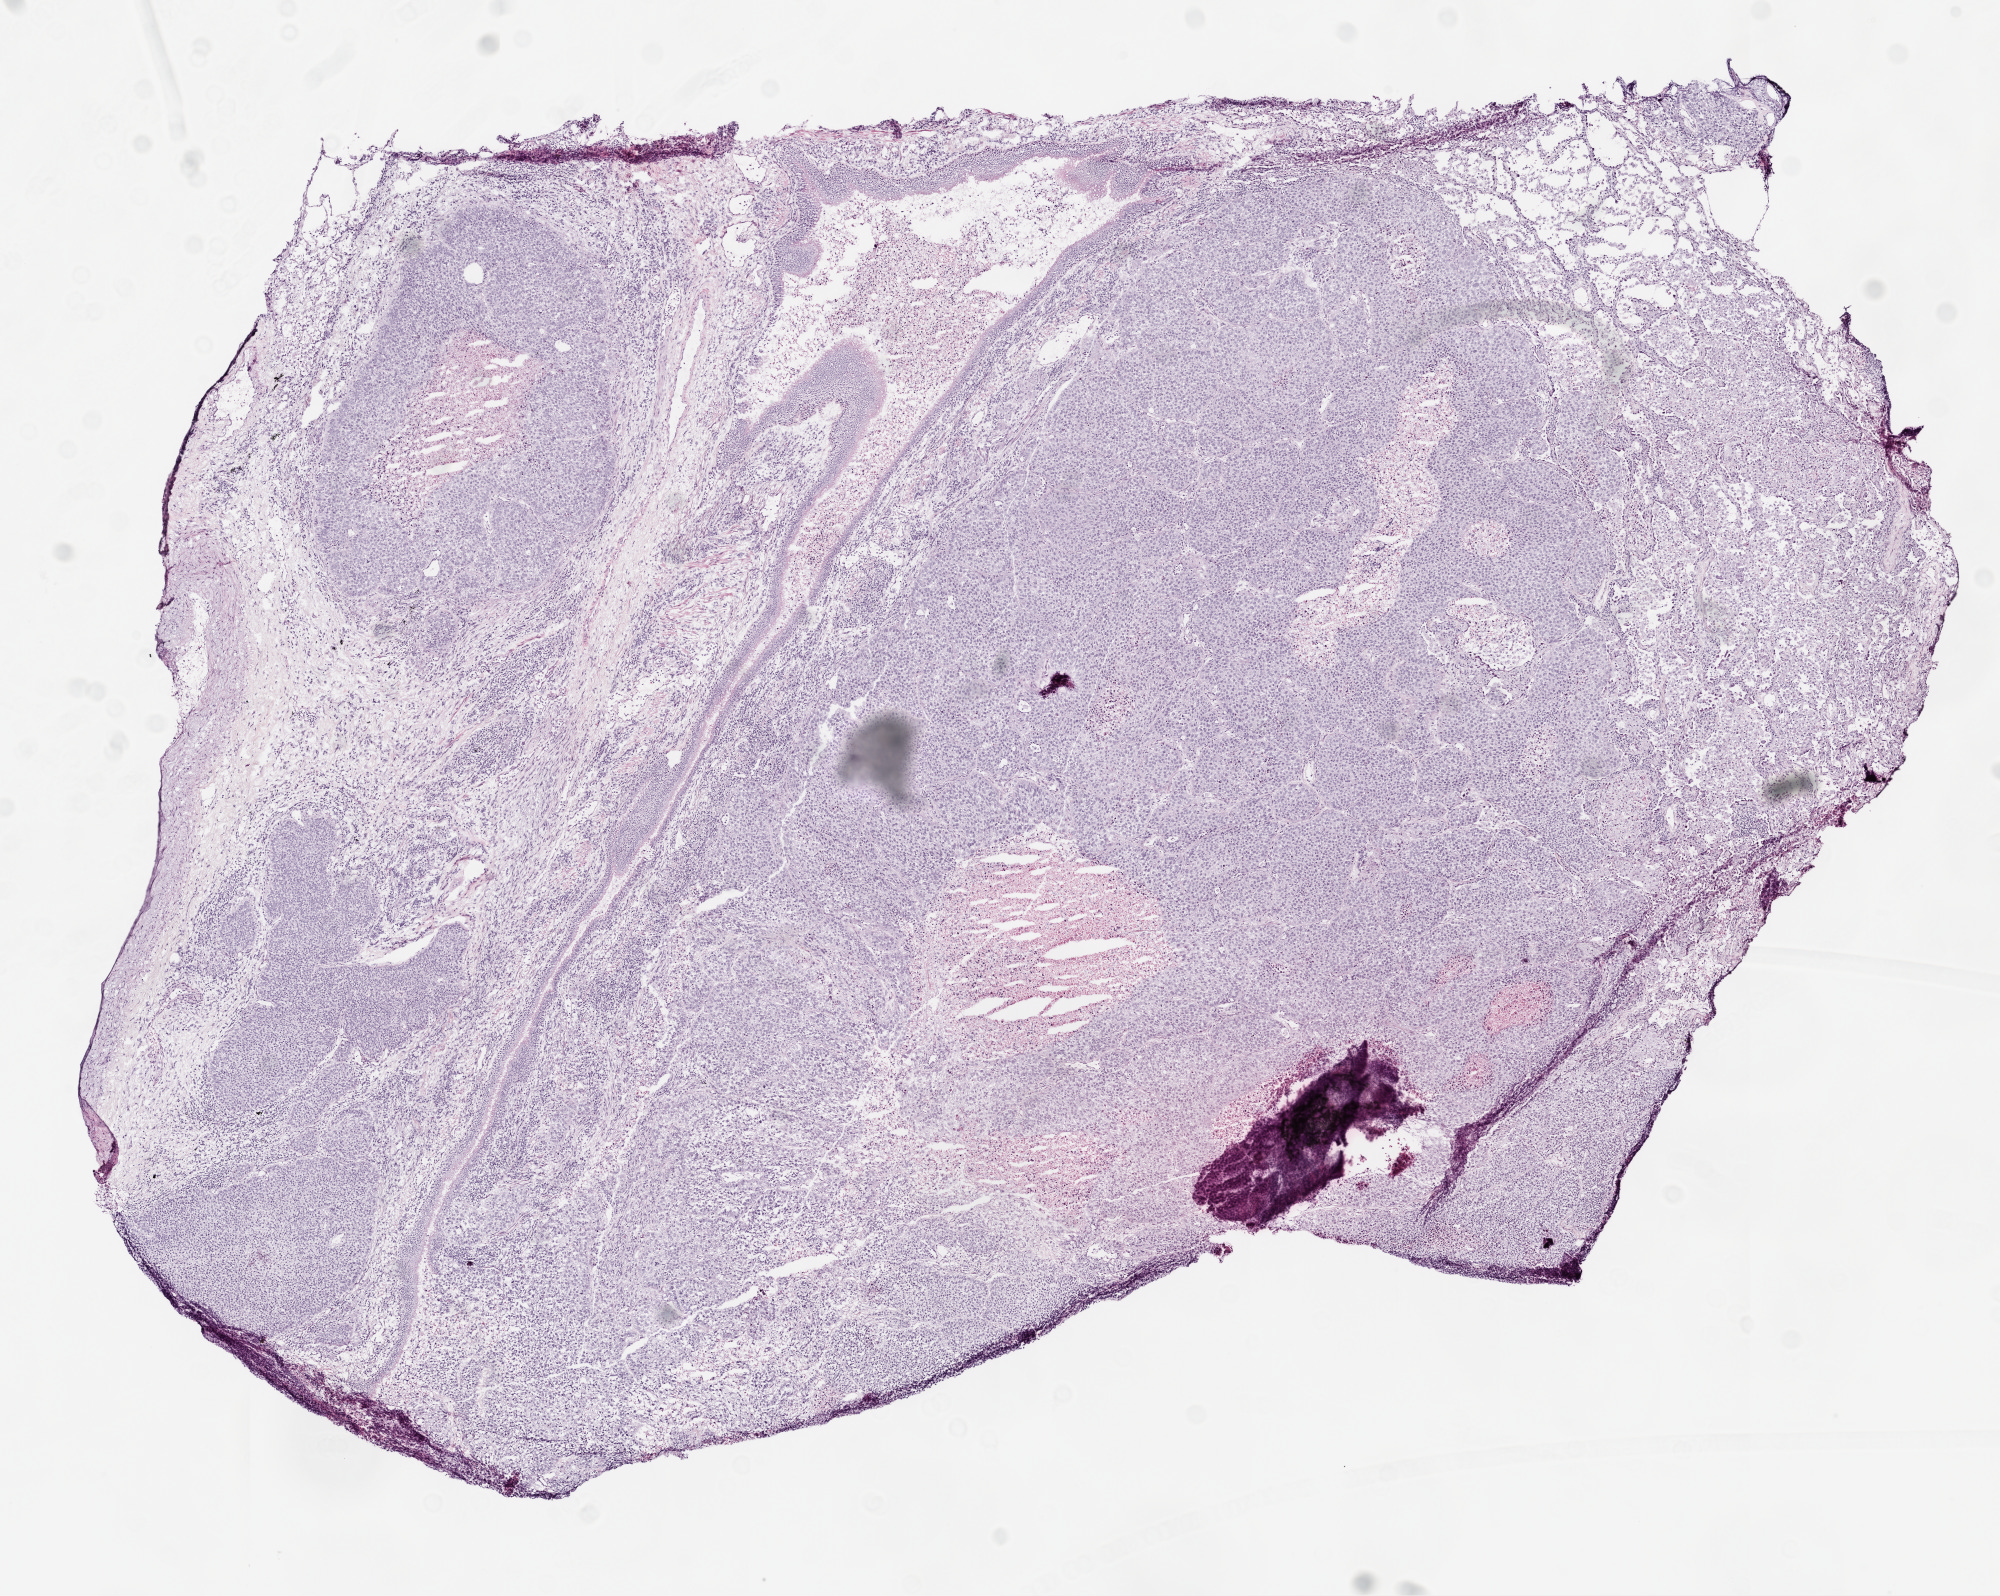
H&E whole-slide image — low-resolution overview of the scanned area, about 8.0 x 6.4 mm, frozen section from the top of the tissue portion, sample: primary tumour, lung. Female, age 83 years at initial diagnosis. Composition of this section per pathologist review: tumour cells 73%, tumour nuclei 80%, normal cells 15%, stromal cells 5%, necrosis 7%.
Laterality: right. AJCC pathologic stage: IB. Histologic diagnosis: Squamous cell carcinoma, NOS.